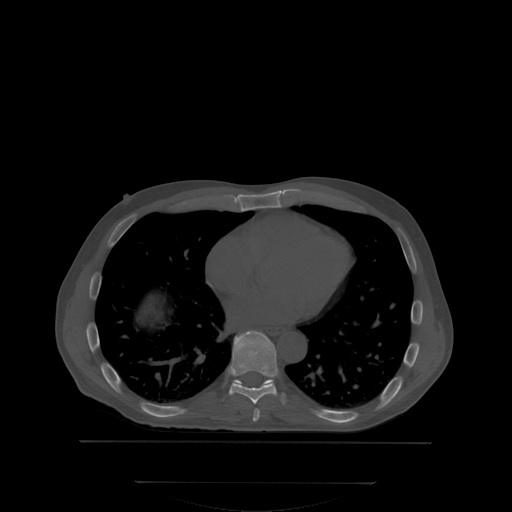
CT including the spine, one axial slice; position 214 of 350 along the scan axis; bone window (W 1800 / L 400 HU); 2.5 mm slice thickness; 512 × 512 image matrix, field of view 500 × 500 mm. Male patient, age 58 years. Case-level facts recorded for this patient, not image findings: primary cancer: prostate.
Outlined on this slice (semi-automatic segmentation, software-assisted and operator-edited):
- T7 vertebra: bounding box [x1, y1, x2, y2] px = [253, 409, 259, 420]
- T8 vertebra: [228, 332, 278, 403]
- T9 vertebra: [266, 381, 271, 383]